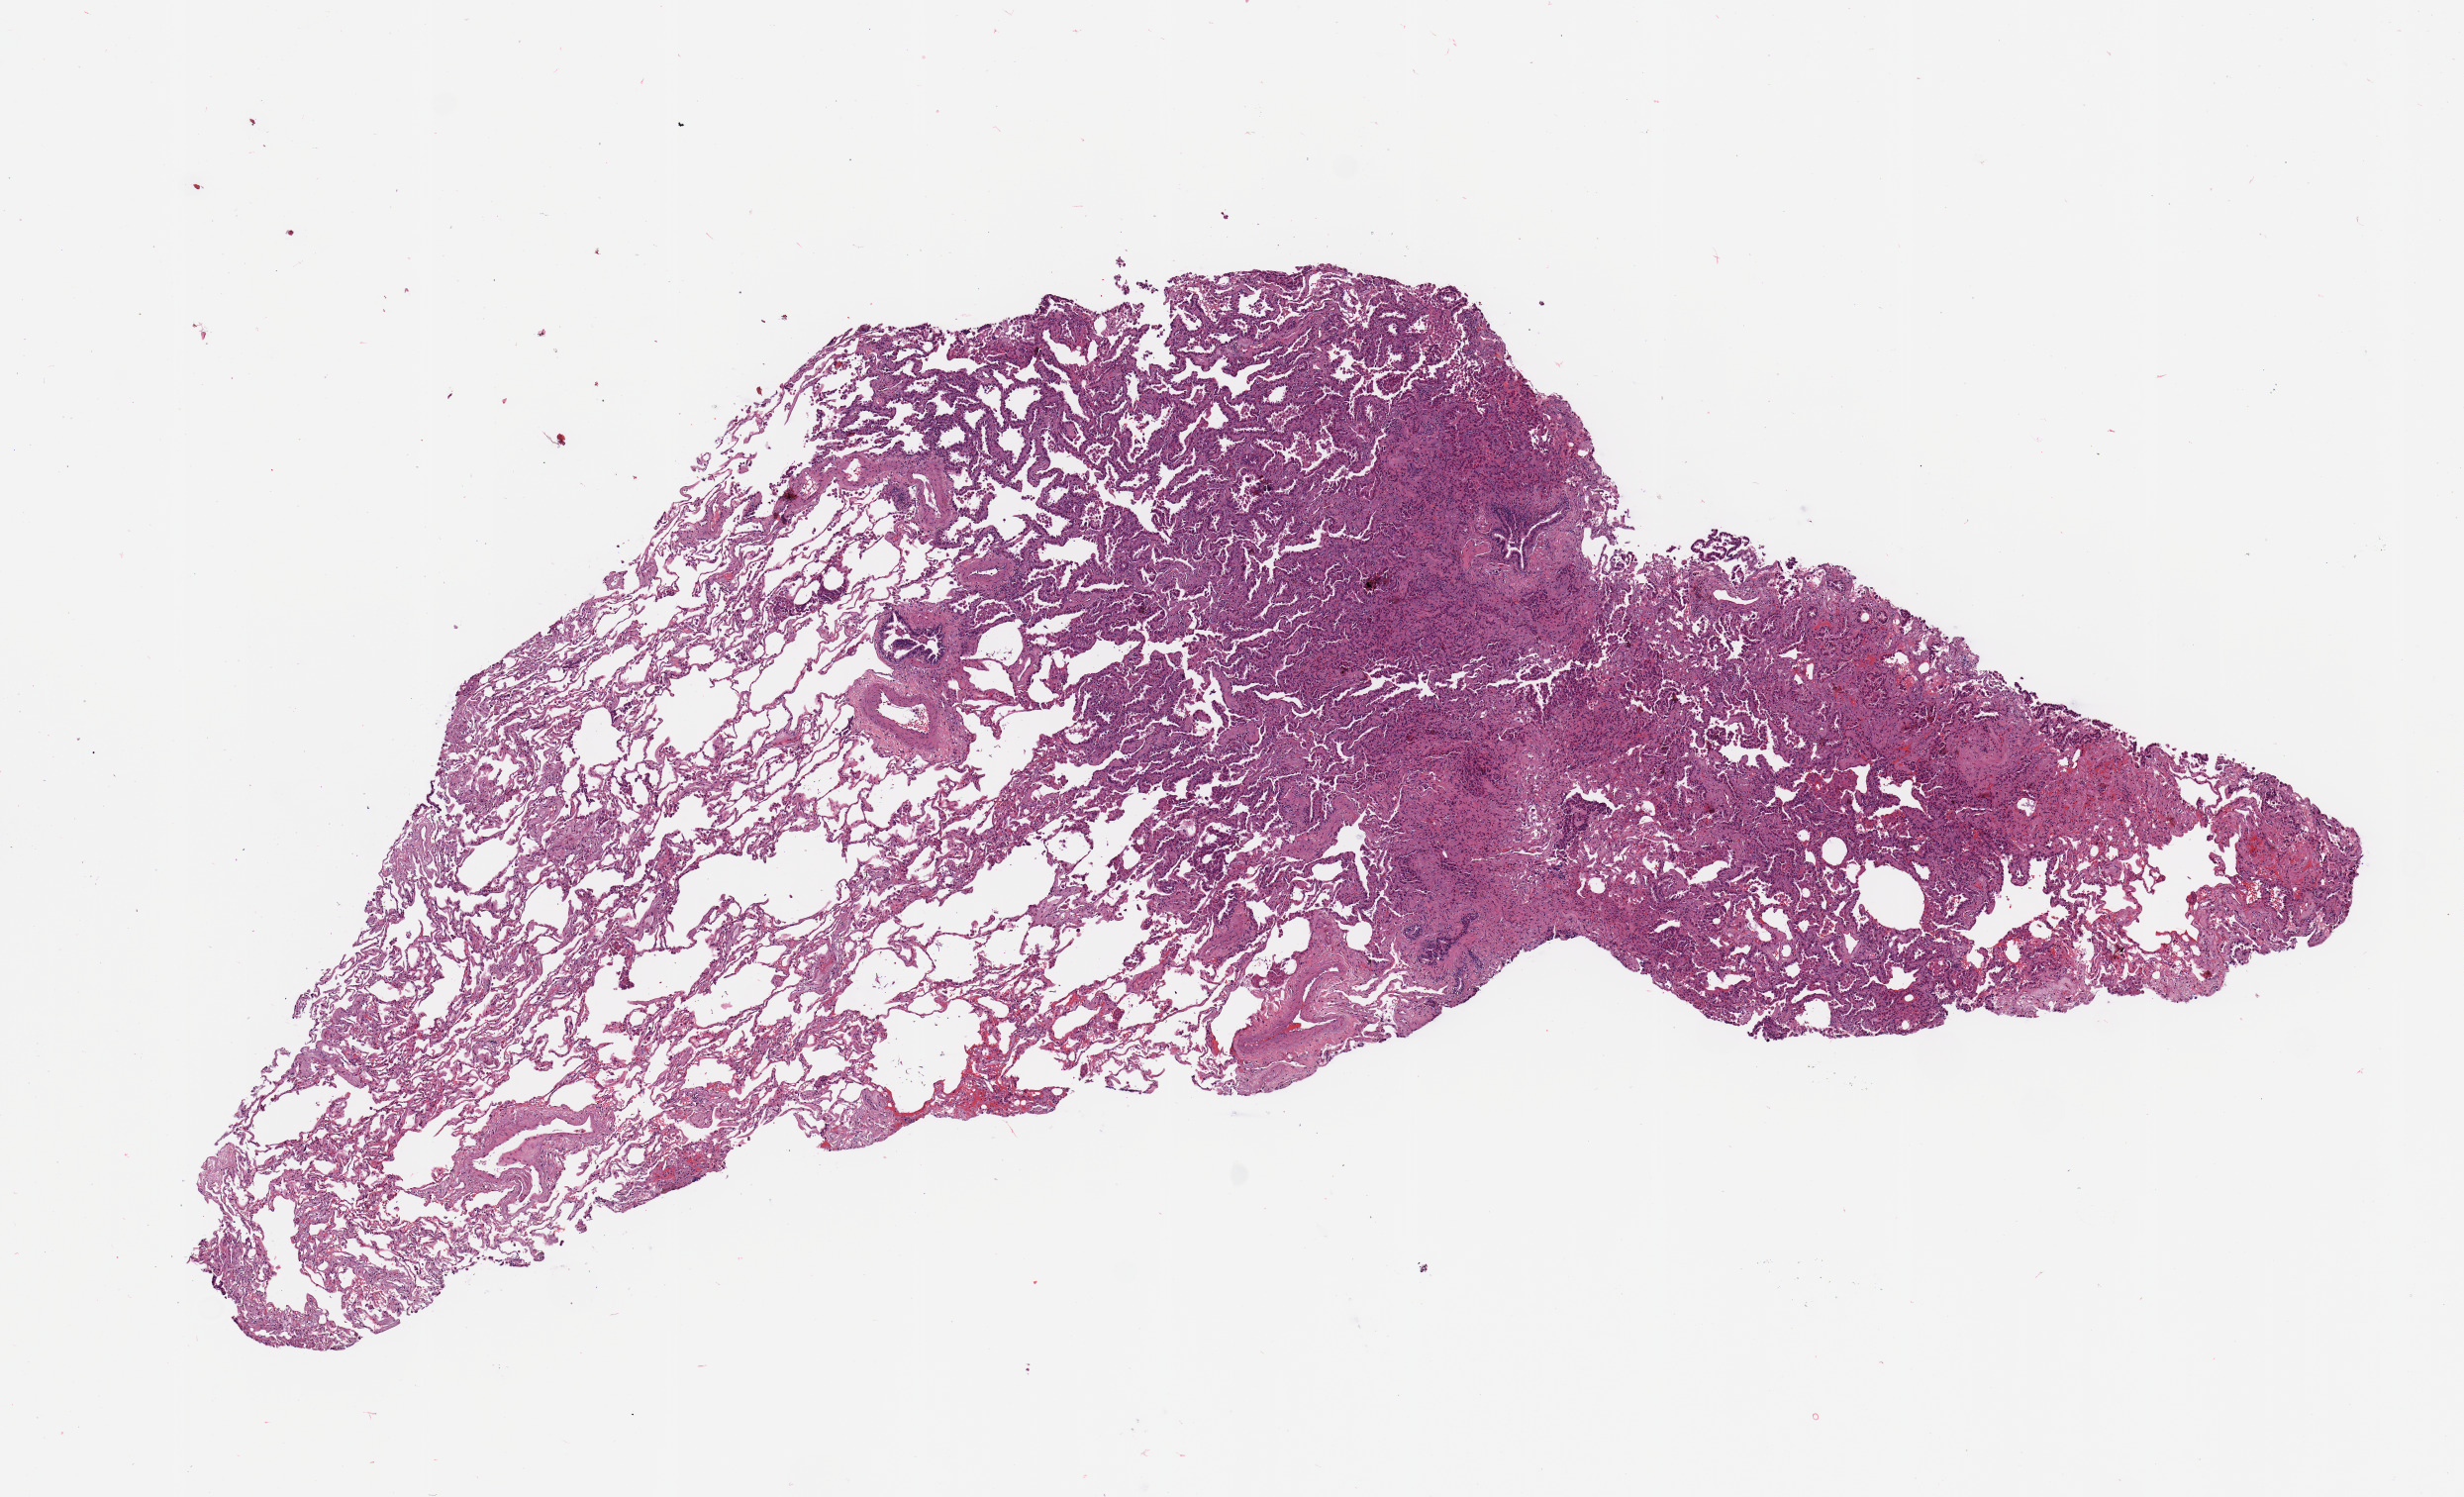
Whole-slide histology image, H&E, shown as a low-resolution overview of the whole scanned area (about 9.8 x 6.0 mm), lung, tumour tissue. 68-year-old female patient. Histologic grade: G2 (moderately differentiated).
• histologic diagnosis: Adenocarcinoma, NOS
• primary tumour site (as recorded): left upper lobe
• AJCC pathologic stage: IA